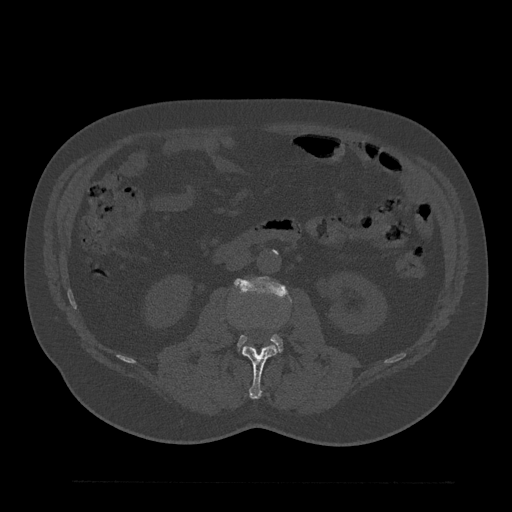
CT including the spine, one axial slice. Bone window (W 1800 / L 400 HU). 512 × 512 image matrix. Patient: male, 61 years. Case-level facts recorded for this patient, not image findings: primary cancer: prostate.
Annotated regions visible in this slice (semi-automatically segmented with operator editing):
- L2 vertebra: bounding box (x1, y1, x2, y2) in pixels: (242, 327, 276, 399)
- L3 vertebra: (235, 277, 287, 351)